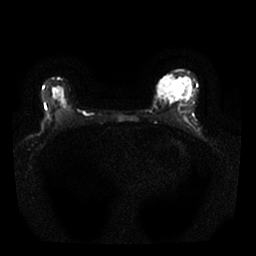
Breast MRI, one axial slice; slice 16 of 25 in the series (ordered by position); diffusion-weighted series; image 2 of 4 stored at this slice position (different b-values; order by instance number); 1.5 T; 4 mm slice thickness; 256 × 256 image matrix, field of view 310 × 310 mm. Female patient.
Annotated regions visible in this slice (outlined manually by an expert reader):
- tumour on diffusion-weighted imaging: bounding box <160,77,182,100> (left, top, right, bottom; pixels)